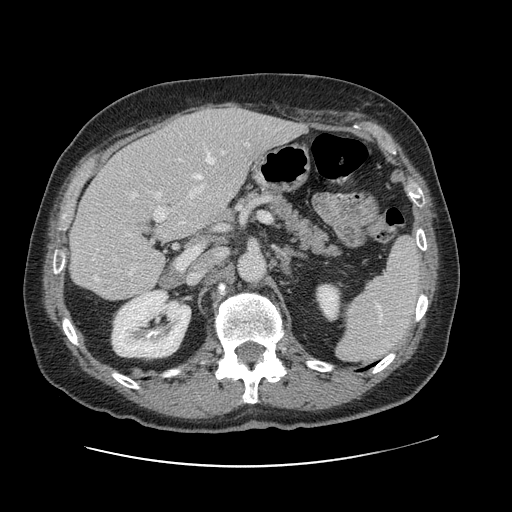
Contrast-enhanced abdominal CT, one axial slice; position 62 of 138 along the scan axis; 120 kVp; intravenous contrast given; soft-tissue window (W 400 / L 40 HU); 512 × 512 image matrix. Male patient, age 71 years. Case-level facts recorded for this patient, not image findings: diagnosis: colorectal cancer liver metastases, imaged before liver resection; multiple liver metastases: no; largest metastasis: 3.3 cm; disease in both lobes: no.
Outlined on this slice (expert manual segmentation):
- hepatic veins: bounding box [x1, y1, x2, y2] px = [92, 152, 227, 281]
- liver: [72, 106, 302, 300]
- planned liver remnant (the part of the liver to remain after resection): [71, 144, 203, 300]
- portal vein (with intrahepatic branches): [97, 143, 249, 250]